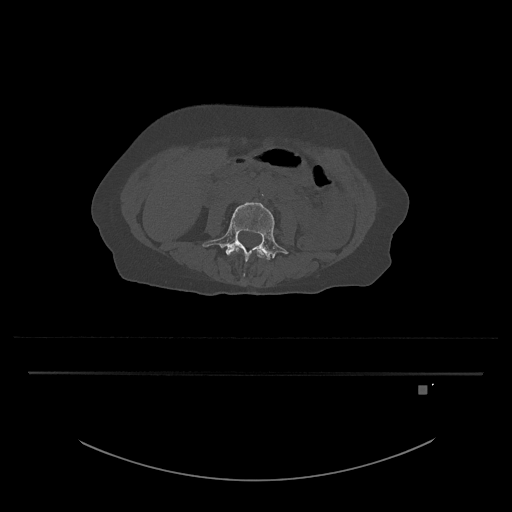
CT including the spine, one axial slice. Slice 374 of 797 in the series (ordered by position). Reconstruction kernel Br40s/3. Bone window (W 1800 / L 400 HU). 0.5 mm slice thickness. 512 × 512 image matrix, field of view 500 × 500 mm. Female patient, age 57 years. From the clinical record (not read from this slice): primary cancer: cervical.
Outlined on this slice (semi-automatic segmentation, software-assisted and operator-edited):
- L3 vertebra: box from (x=237, y=250) to (x=265, y=258) px
- L4 vertebra: (x=202, y=202)–(x=288, y=262)